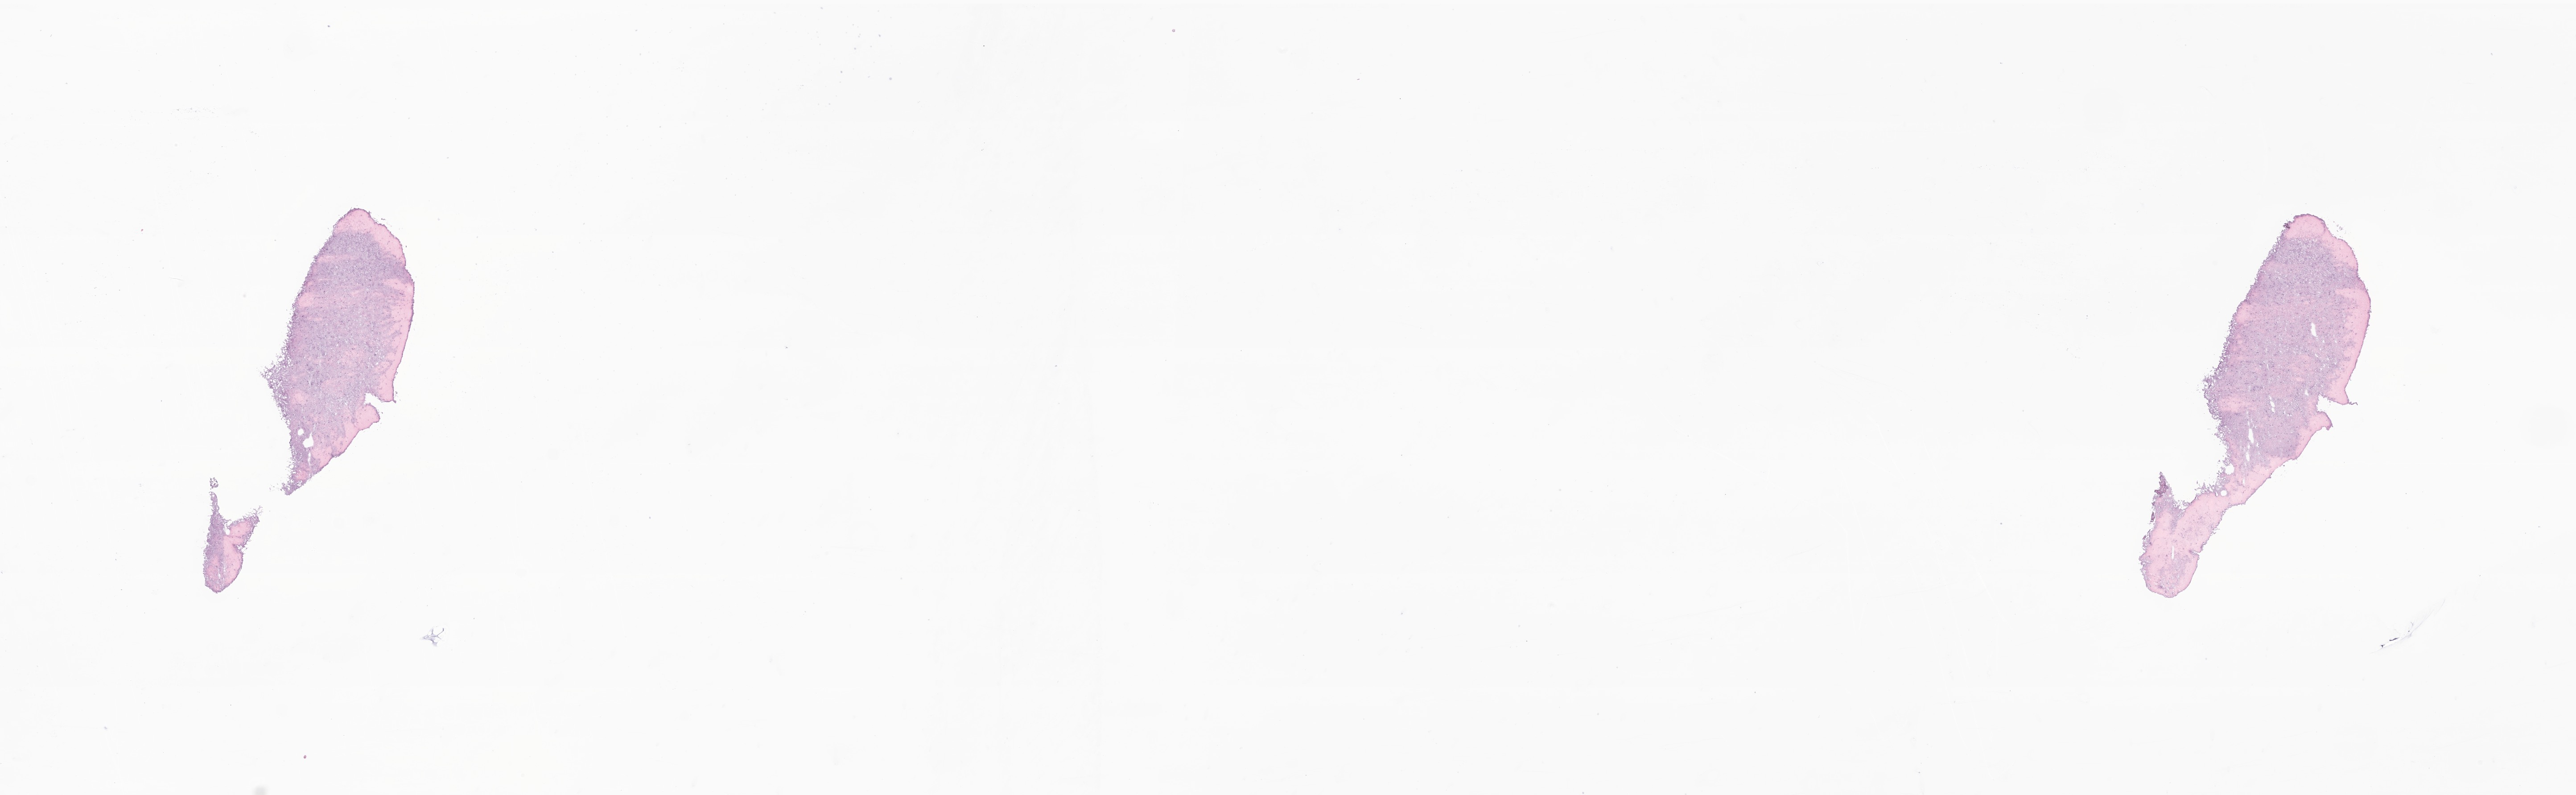
Whole-slide image, H&E stain of tumor tissue from the brain, a low-resolution overview of the entire scanned area, about 24.4 x 7.5 mm. Frozen section. Patient female; age 68 months (5 years 8 months).
Diagnosis (ICD-O-3 morphology term): Neoplasm, malignant.